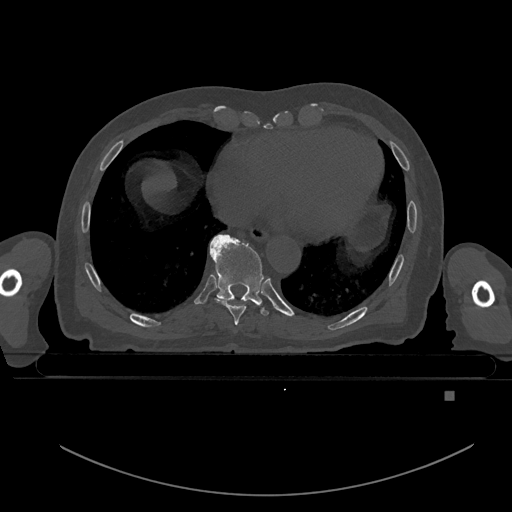
CT including the spine, one axial slice; position 170 of 969 along the scan axis; bone window (W 1800 / L 400 HU); 0.5 mm slice thickness; 512 × 512 image matrix, field of view 456 × 456 mm. Patient: male, 82 years. Case-level facts recorded for this patient, not image findings: primary cancer: prostate; vertebrae with lytic lesions (as recorded): T11, T9, T8, T2.
Structures marked on this image (semi-automatically segmented with operator editing):
- T8 vertebra: box from (x=214, y=297) to (x=252, y=325) px
- T9 vertebra: (x=209, y=235)–(x=269, y=315)